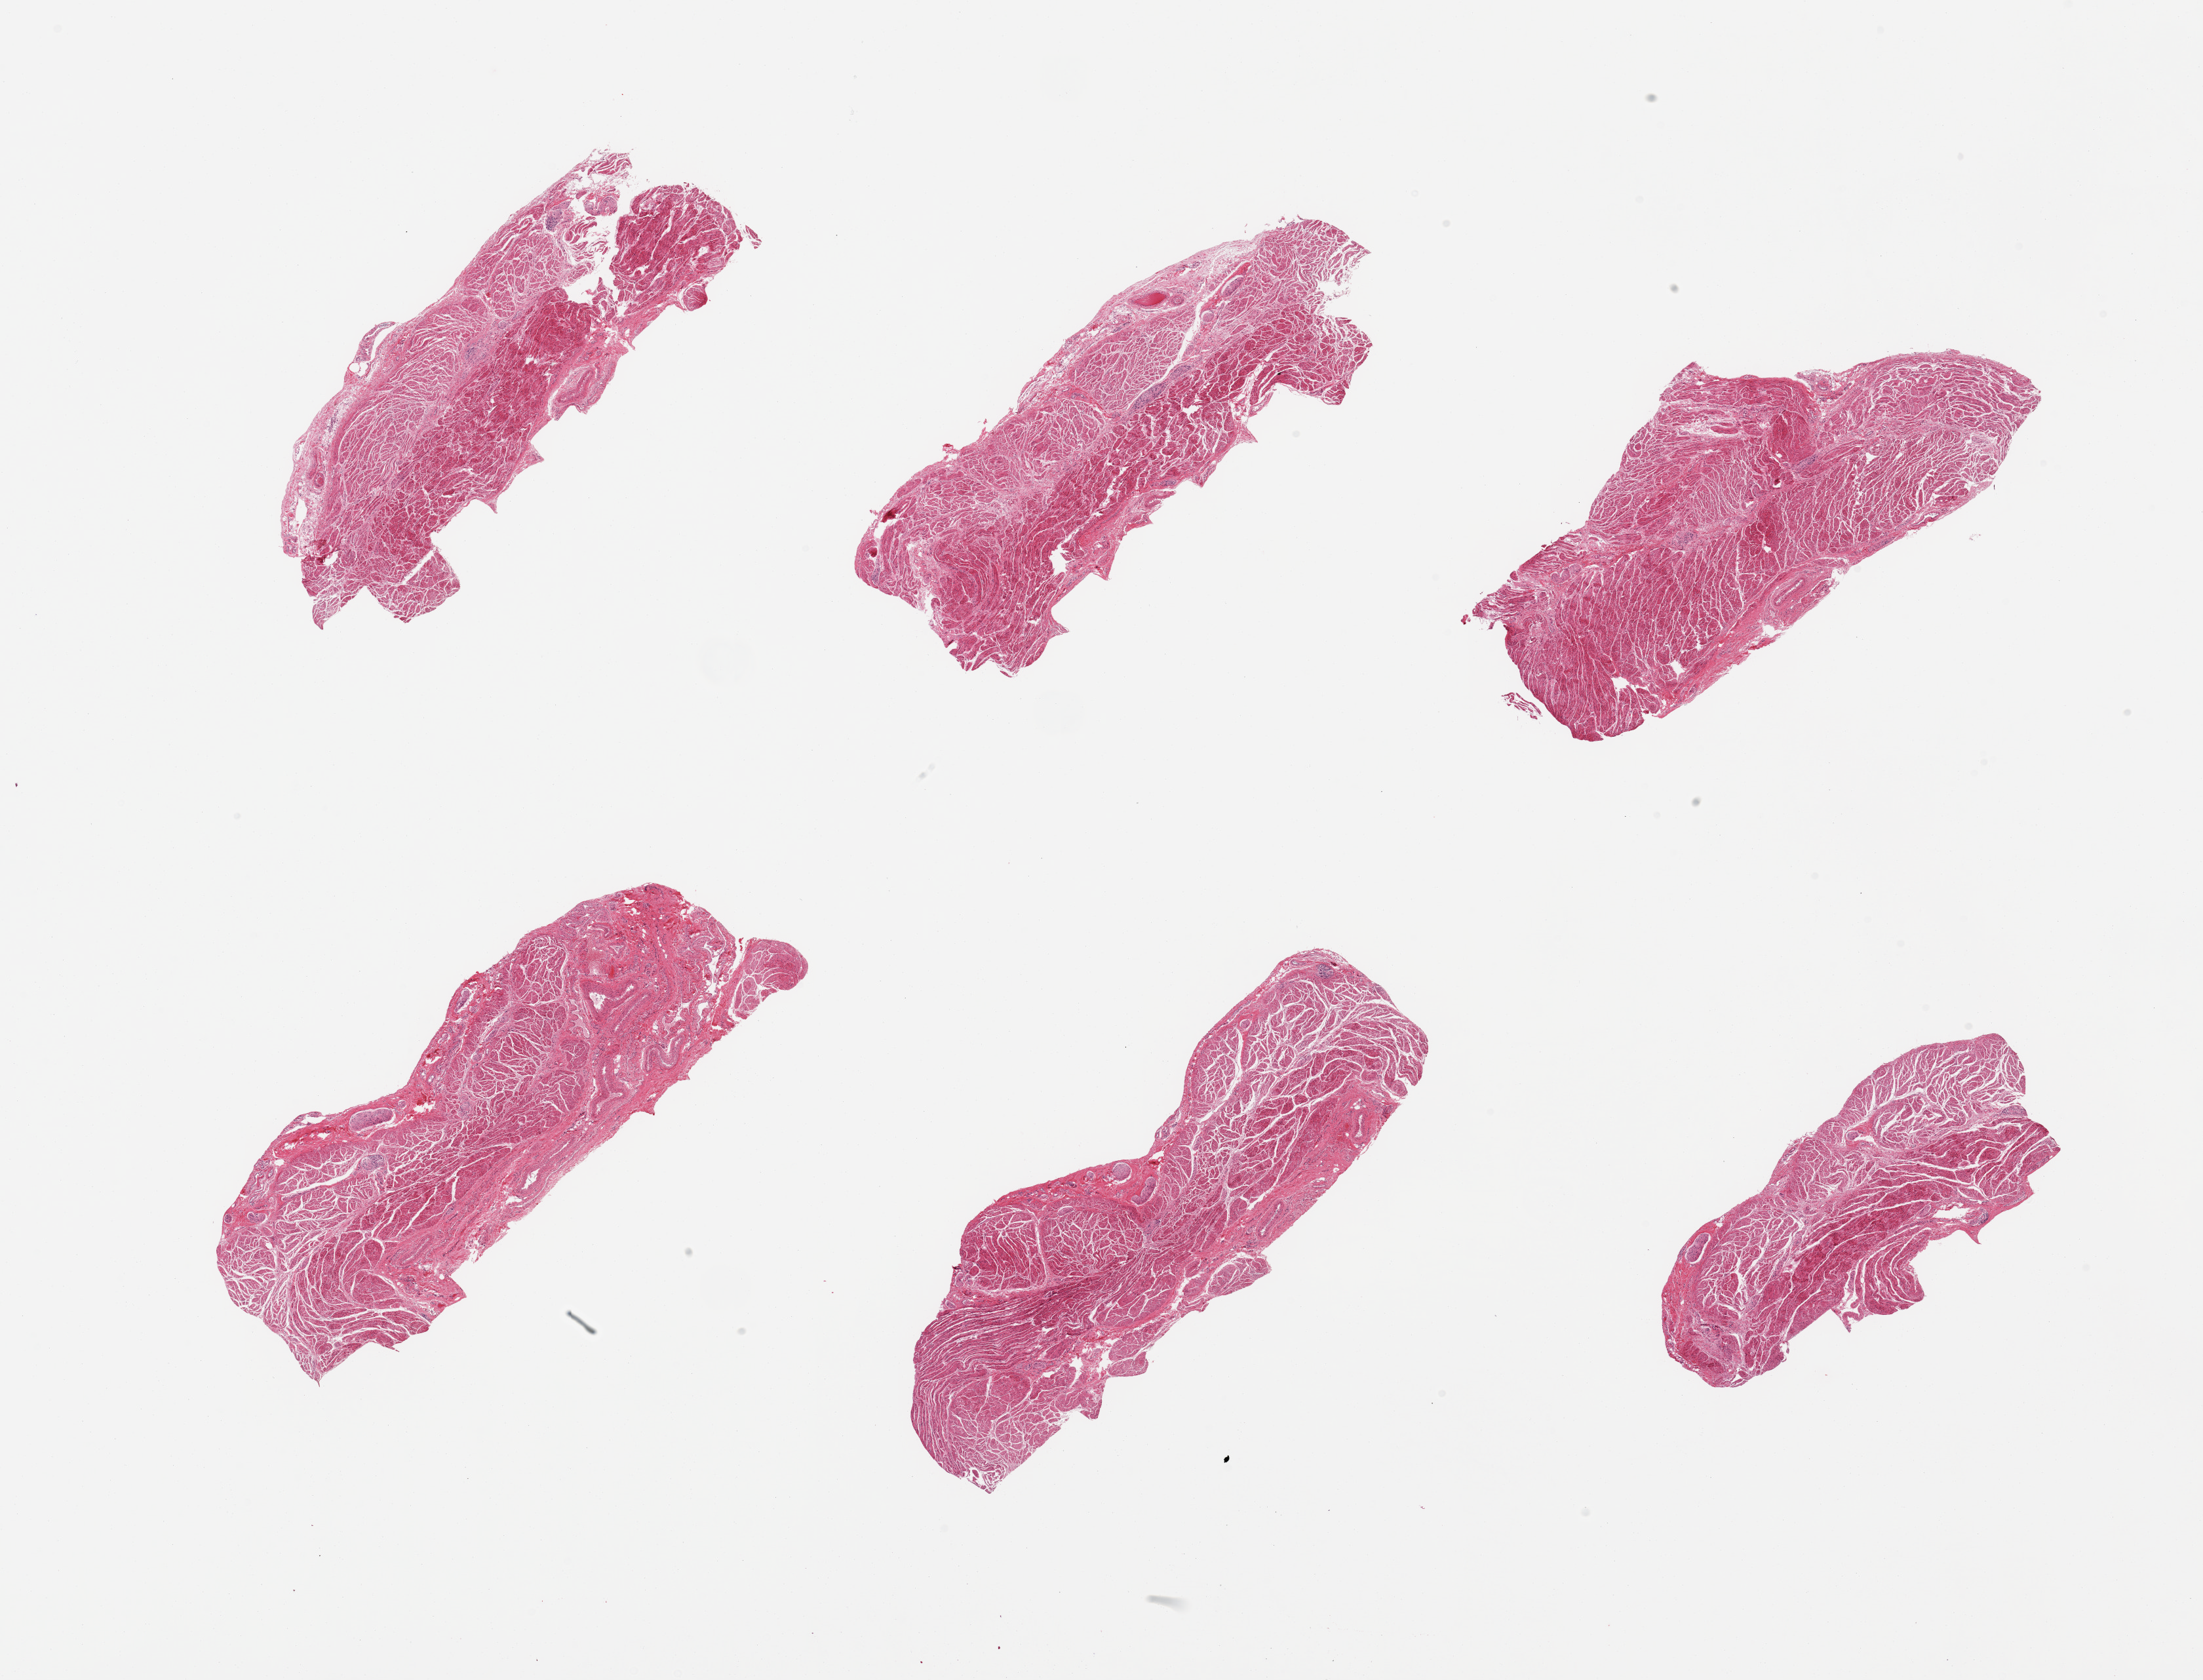
Whole-slide image, hematoxylin and eosin (H&E) stain, a low-resolution overview of the entire scanned area, about 26.6 x 20.3 mm; PAXgene-fixed, paraffin-embedded tissue; sampled site (target tissue): esophageal muscle; tissue donor sample. Donor sex: male.
Reviewer comment on this tissue sample: 6 pieces; owing to probability of gastric origin of 1525, 1625 should be regarded as gastric rather than esophageal; therefore not target tissue.